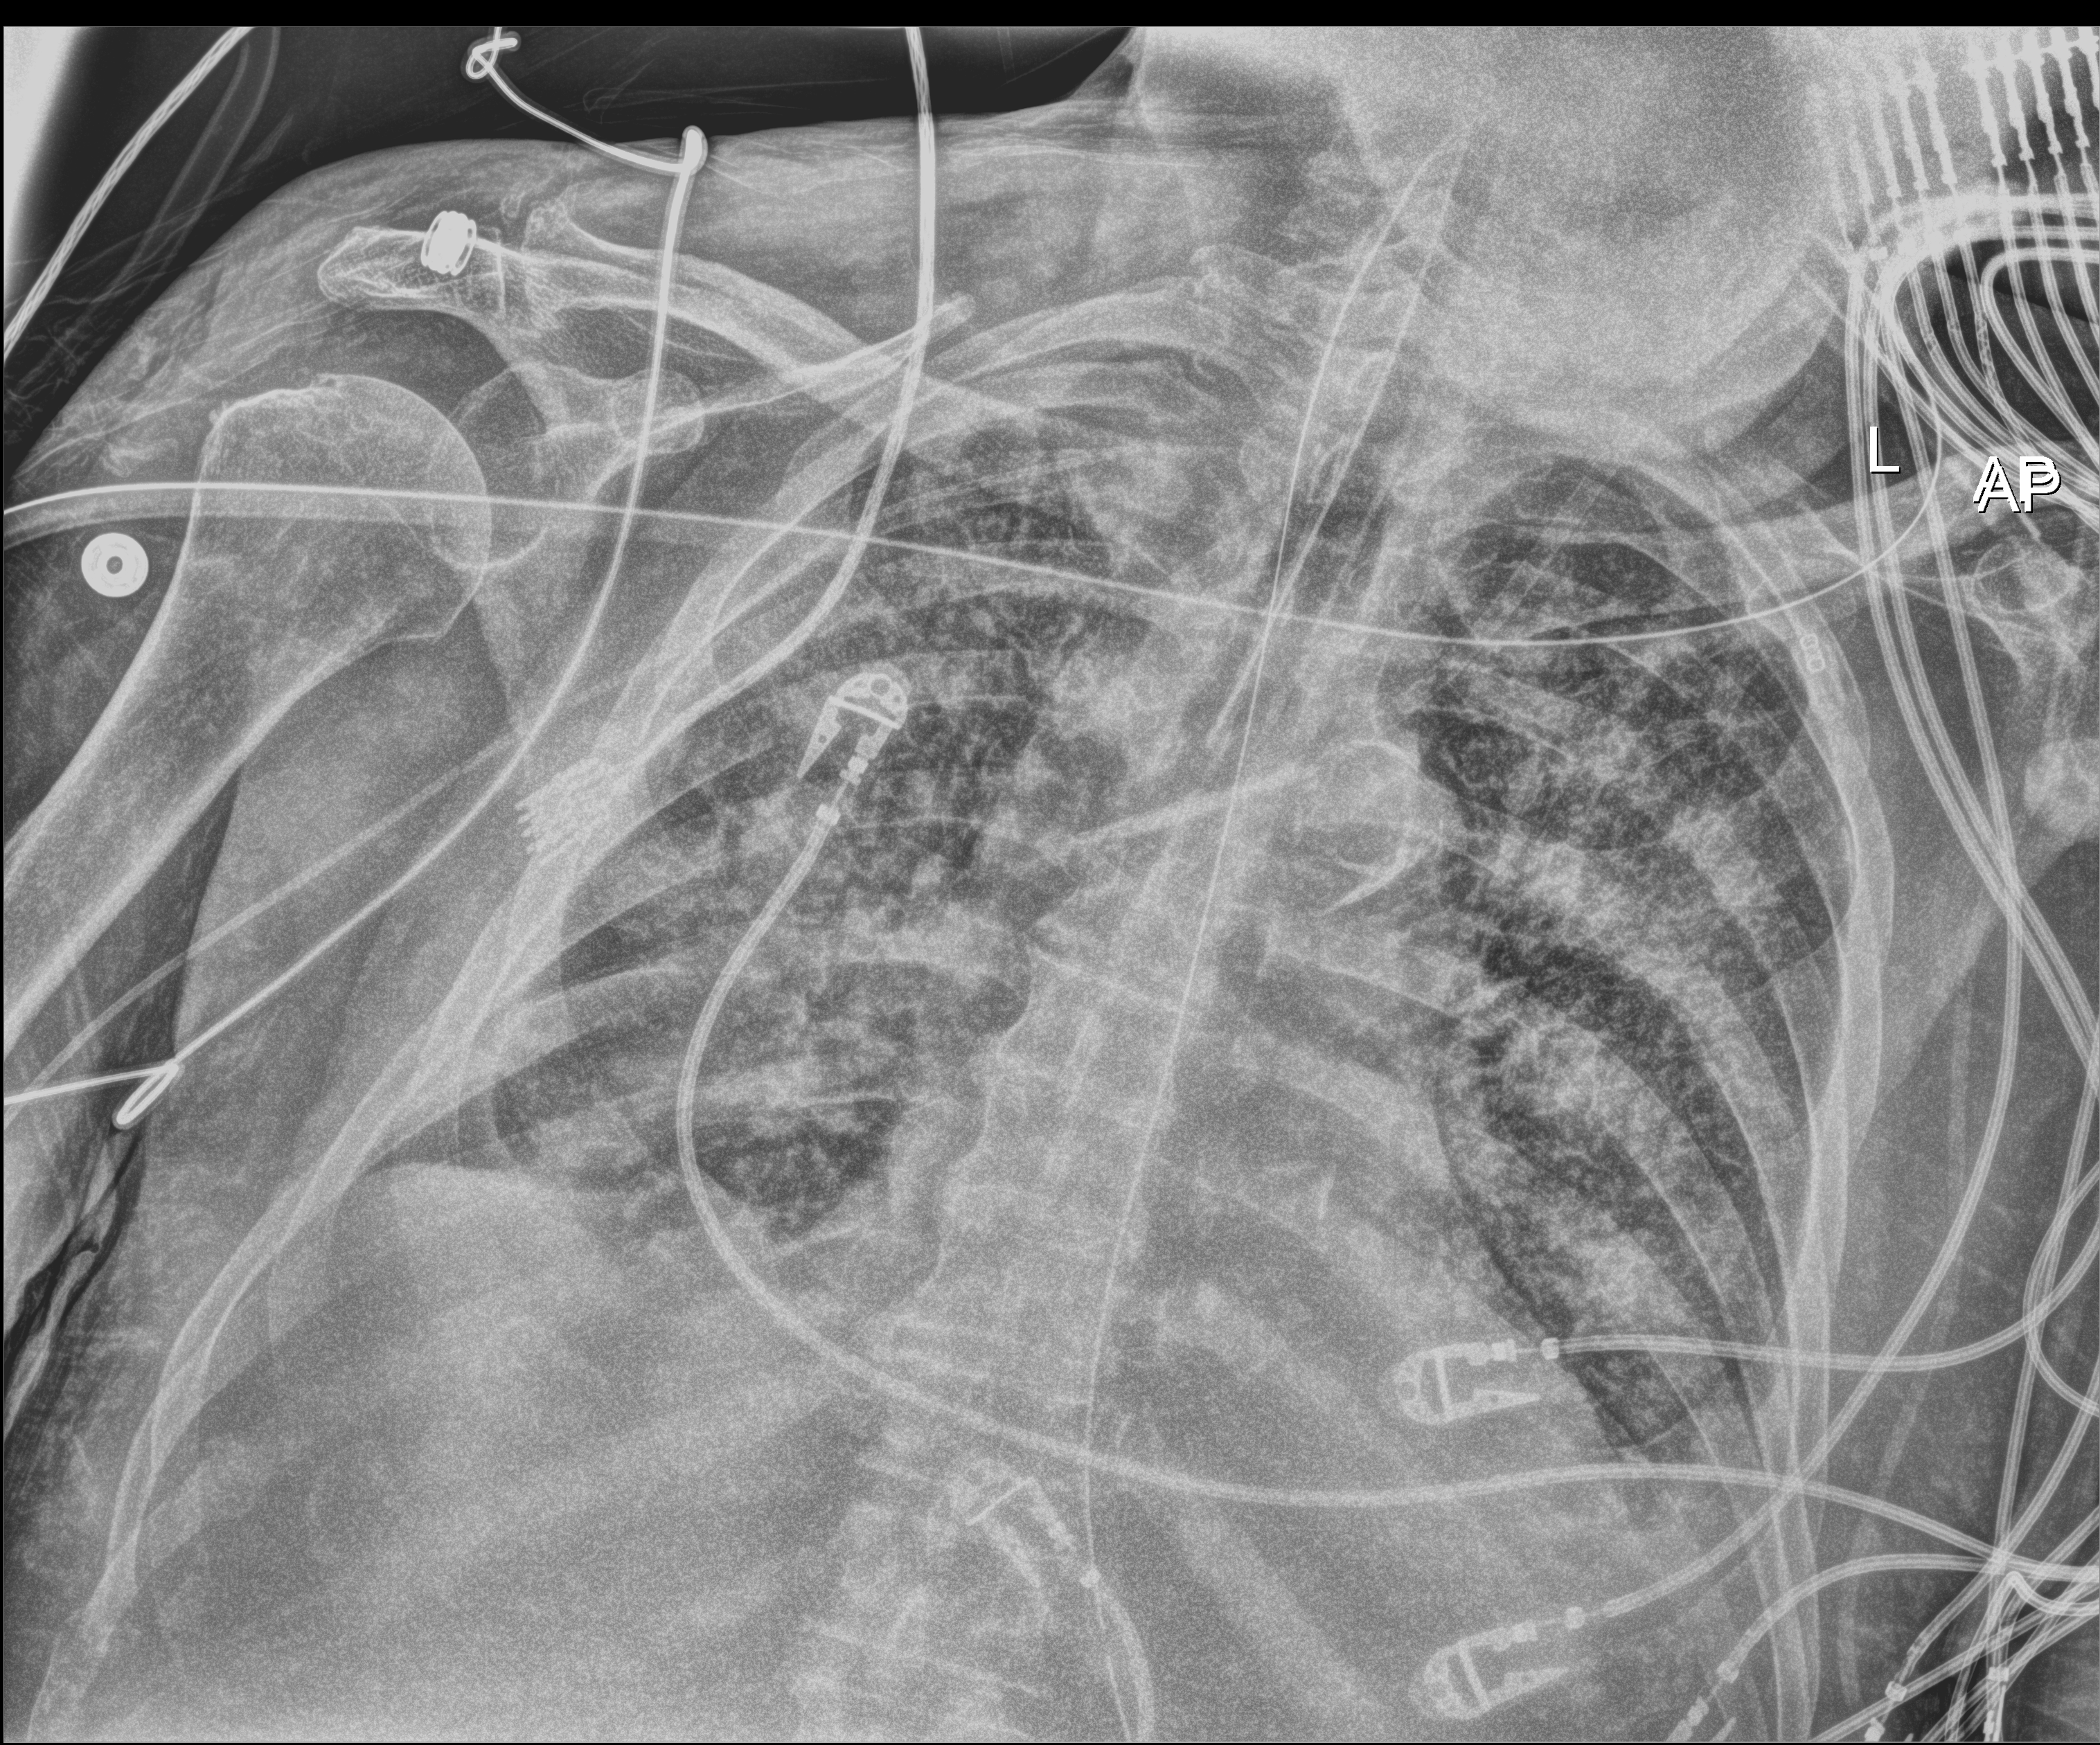
Portable chest radiograph, anteroposterior (AP) projection. Patient hospitalised with COVID-19; male, aged 75–90 years.
From the hospital-stay record, not from the radiograph (when in the stay this image was taken is not recorded): diabetes (admission record): yes; admitted to intensive care during this hospital stay: yes.